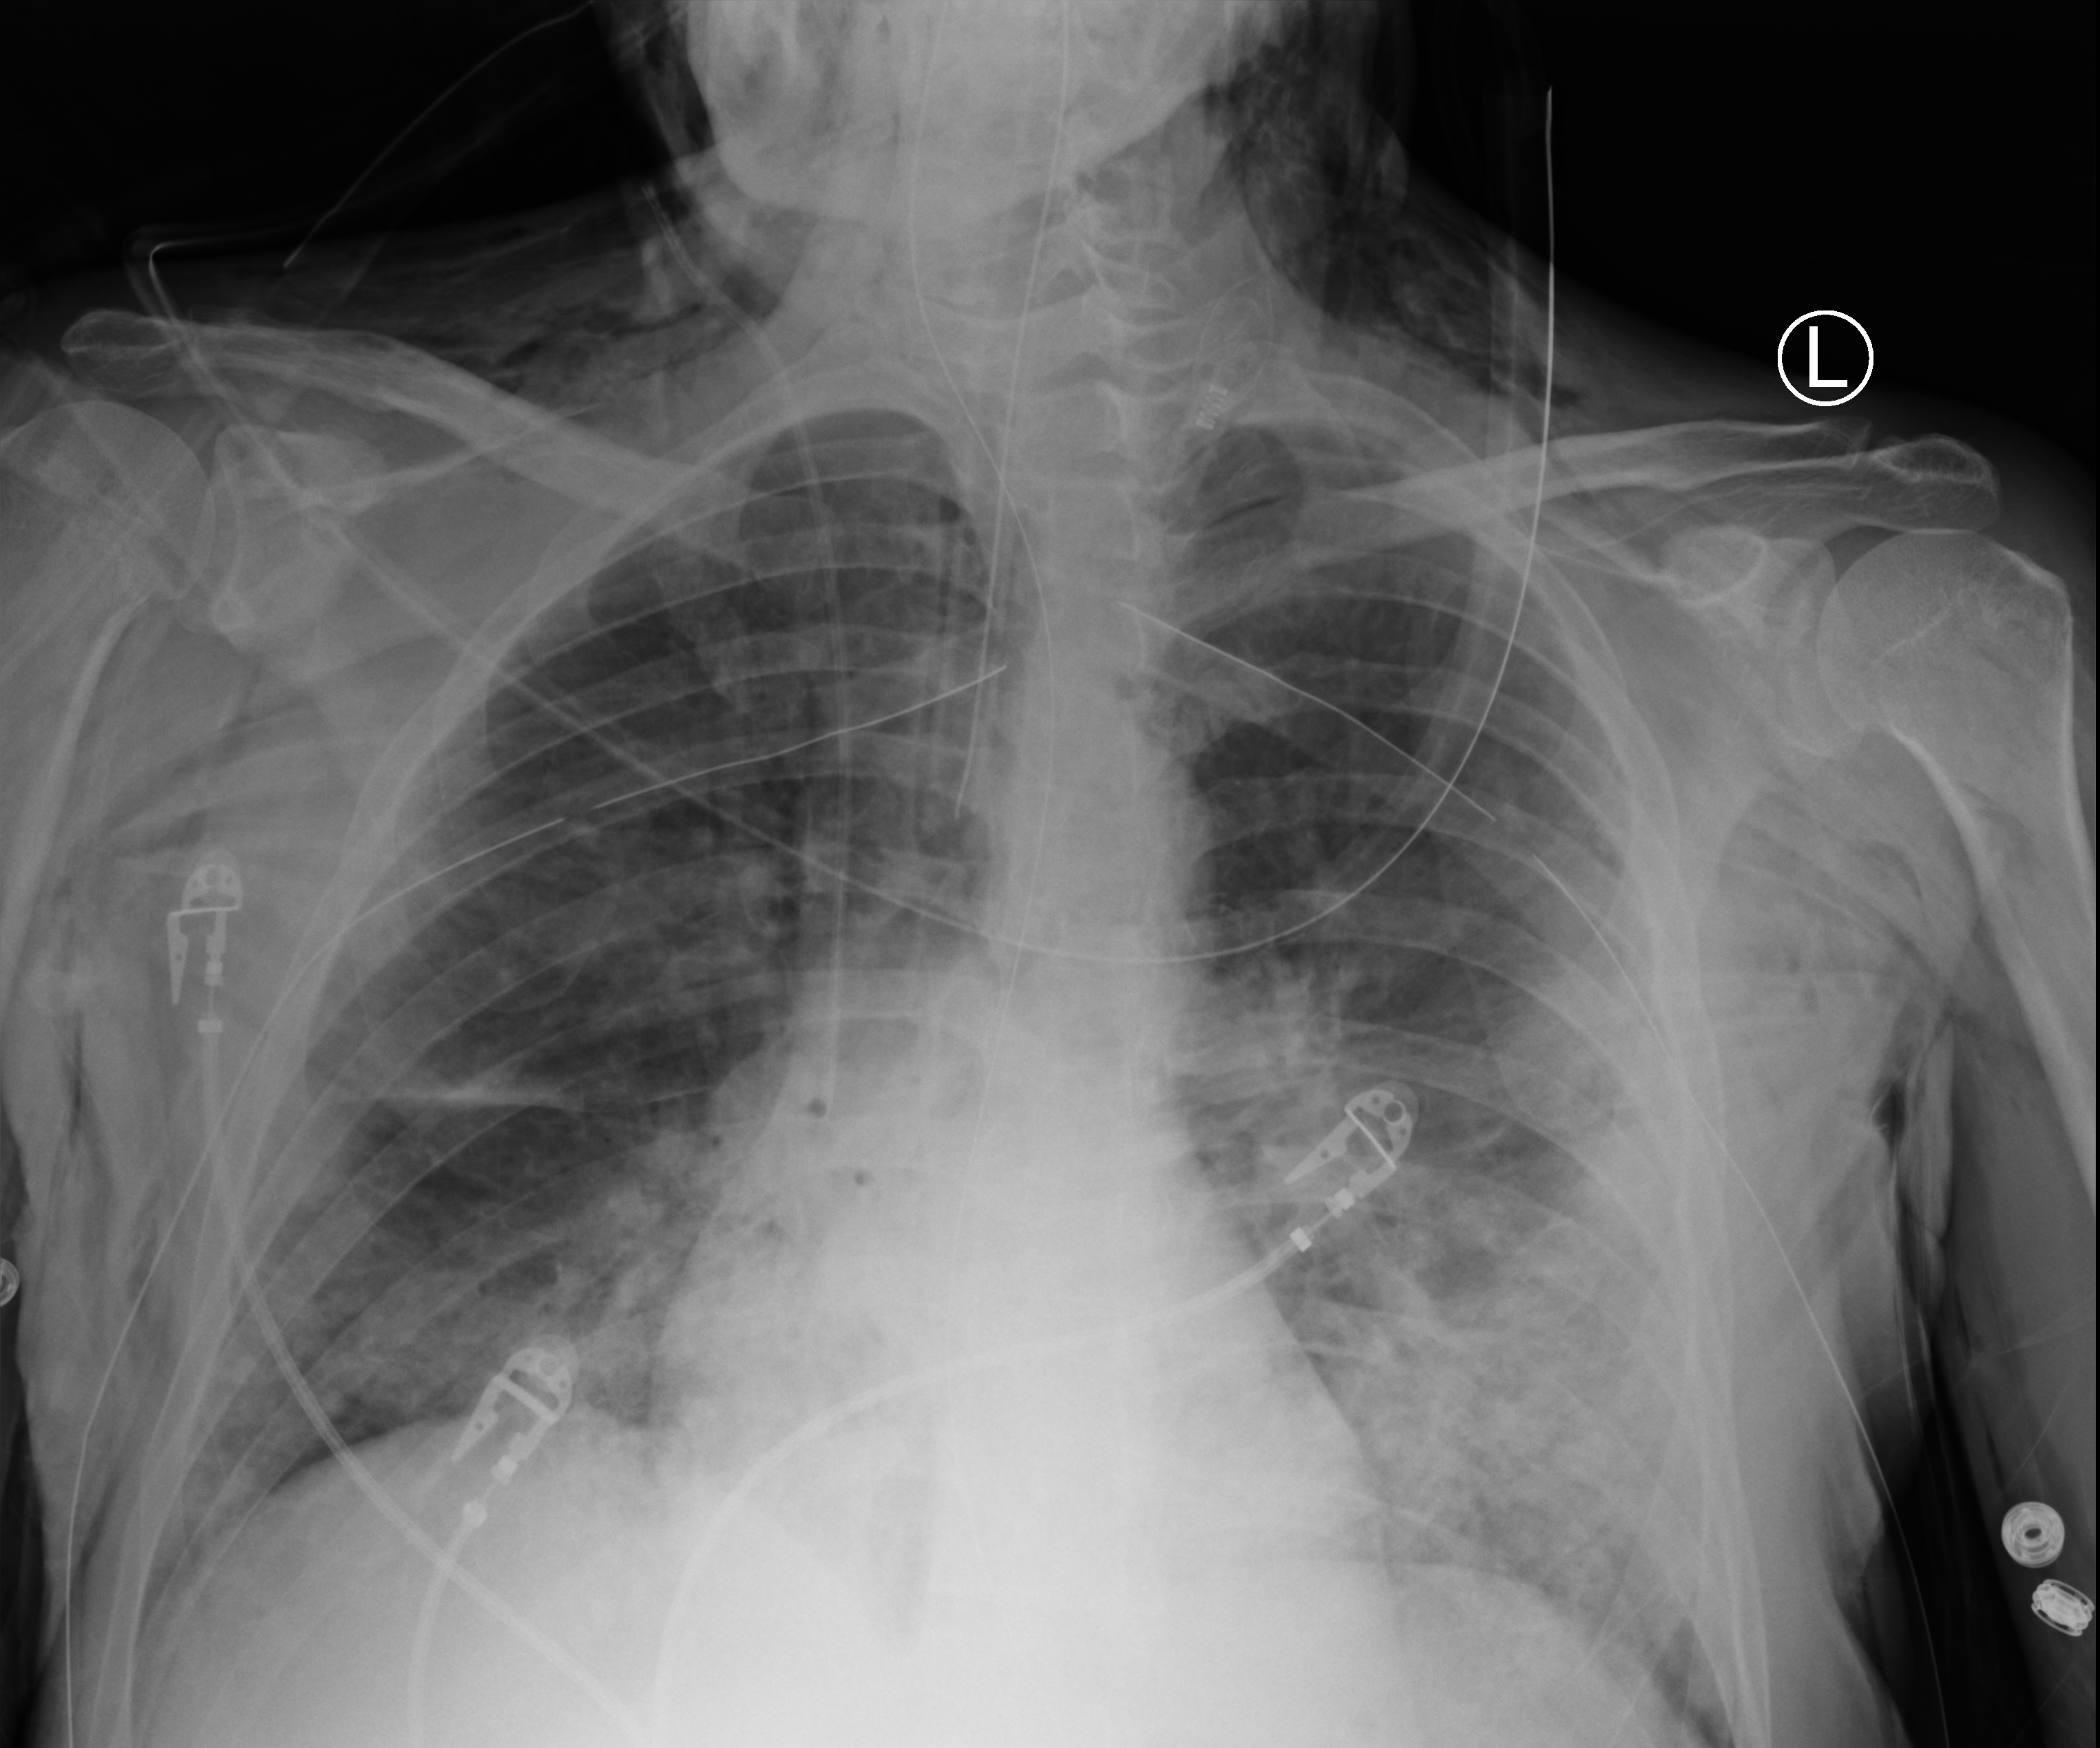
Chest X-ray (portable); anteroposterior (AP) projection. Patient hospitalised with COVID-19; male, aged 18–59 years.
Admission-level facts for this patient (not findings on this image; timing relative to this image not recorded):
- mechanically ventilated during this hospital stay: yes
- admitted to intensive care during this hospital stay: yes